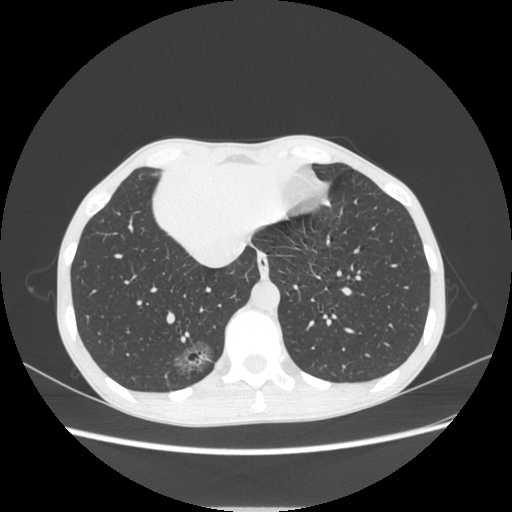
Chest CT, one axial slice. Slice 75 of 272 in the series (ordered by position). 120 kVp. Lung window (W 1500 / L -600 HU). 1.25 mm slice thickness. 512 × 512 image matrix, field of view 350 × 350 mm. Female patient, age 51 years. From the clinical record (not read from this slice): clinical TNM (as recorded): T1c N0 M0.
Annotated regions visible in this slice (rectangle marked by the reading radiologist):
- lung tumour (recorded histology: adenocarcinoma): bounding box (x1, y1, x2, y2) in pixels: (163, 332, 214, 383)